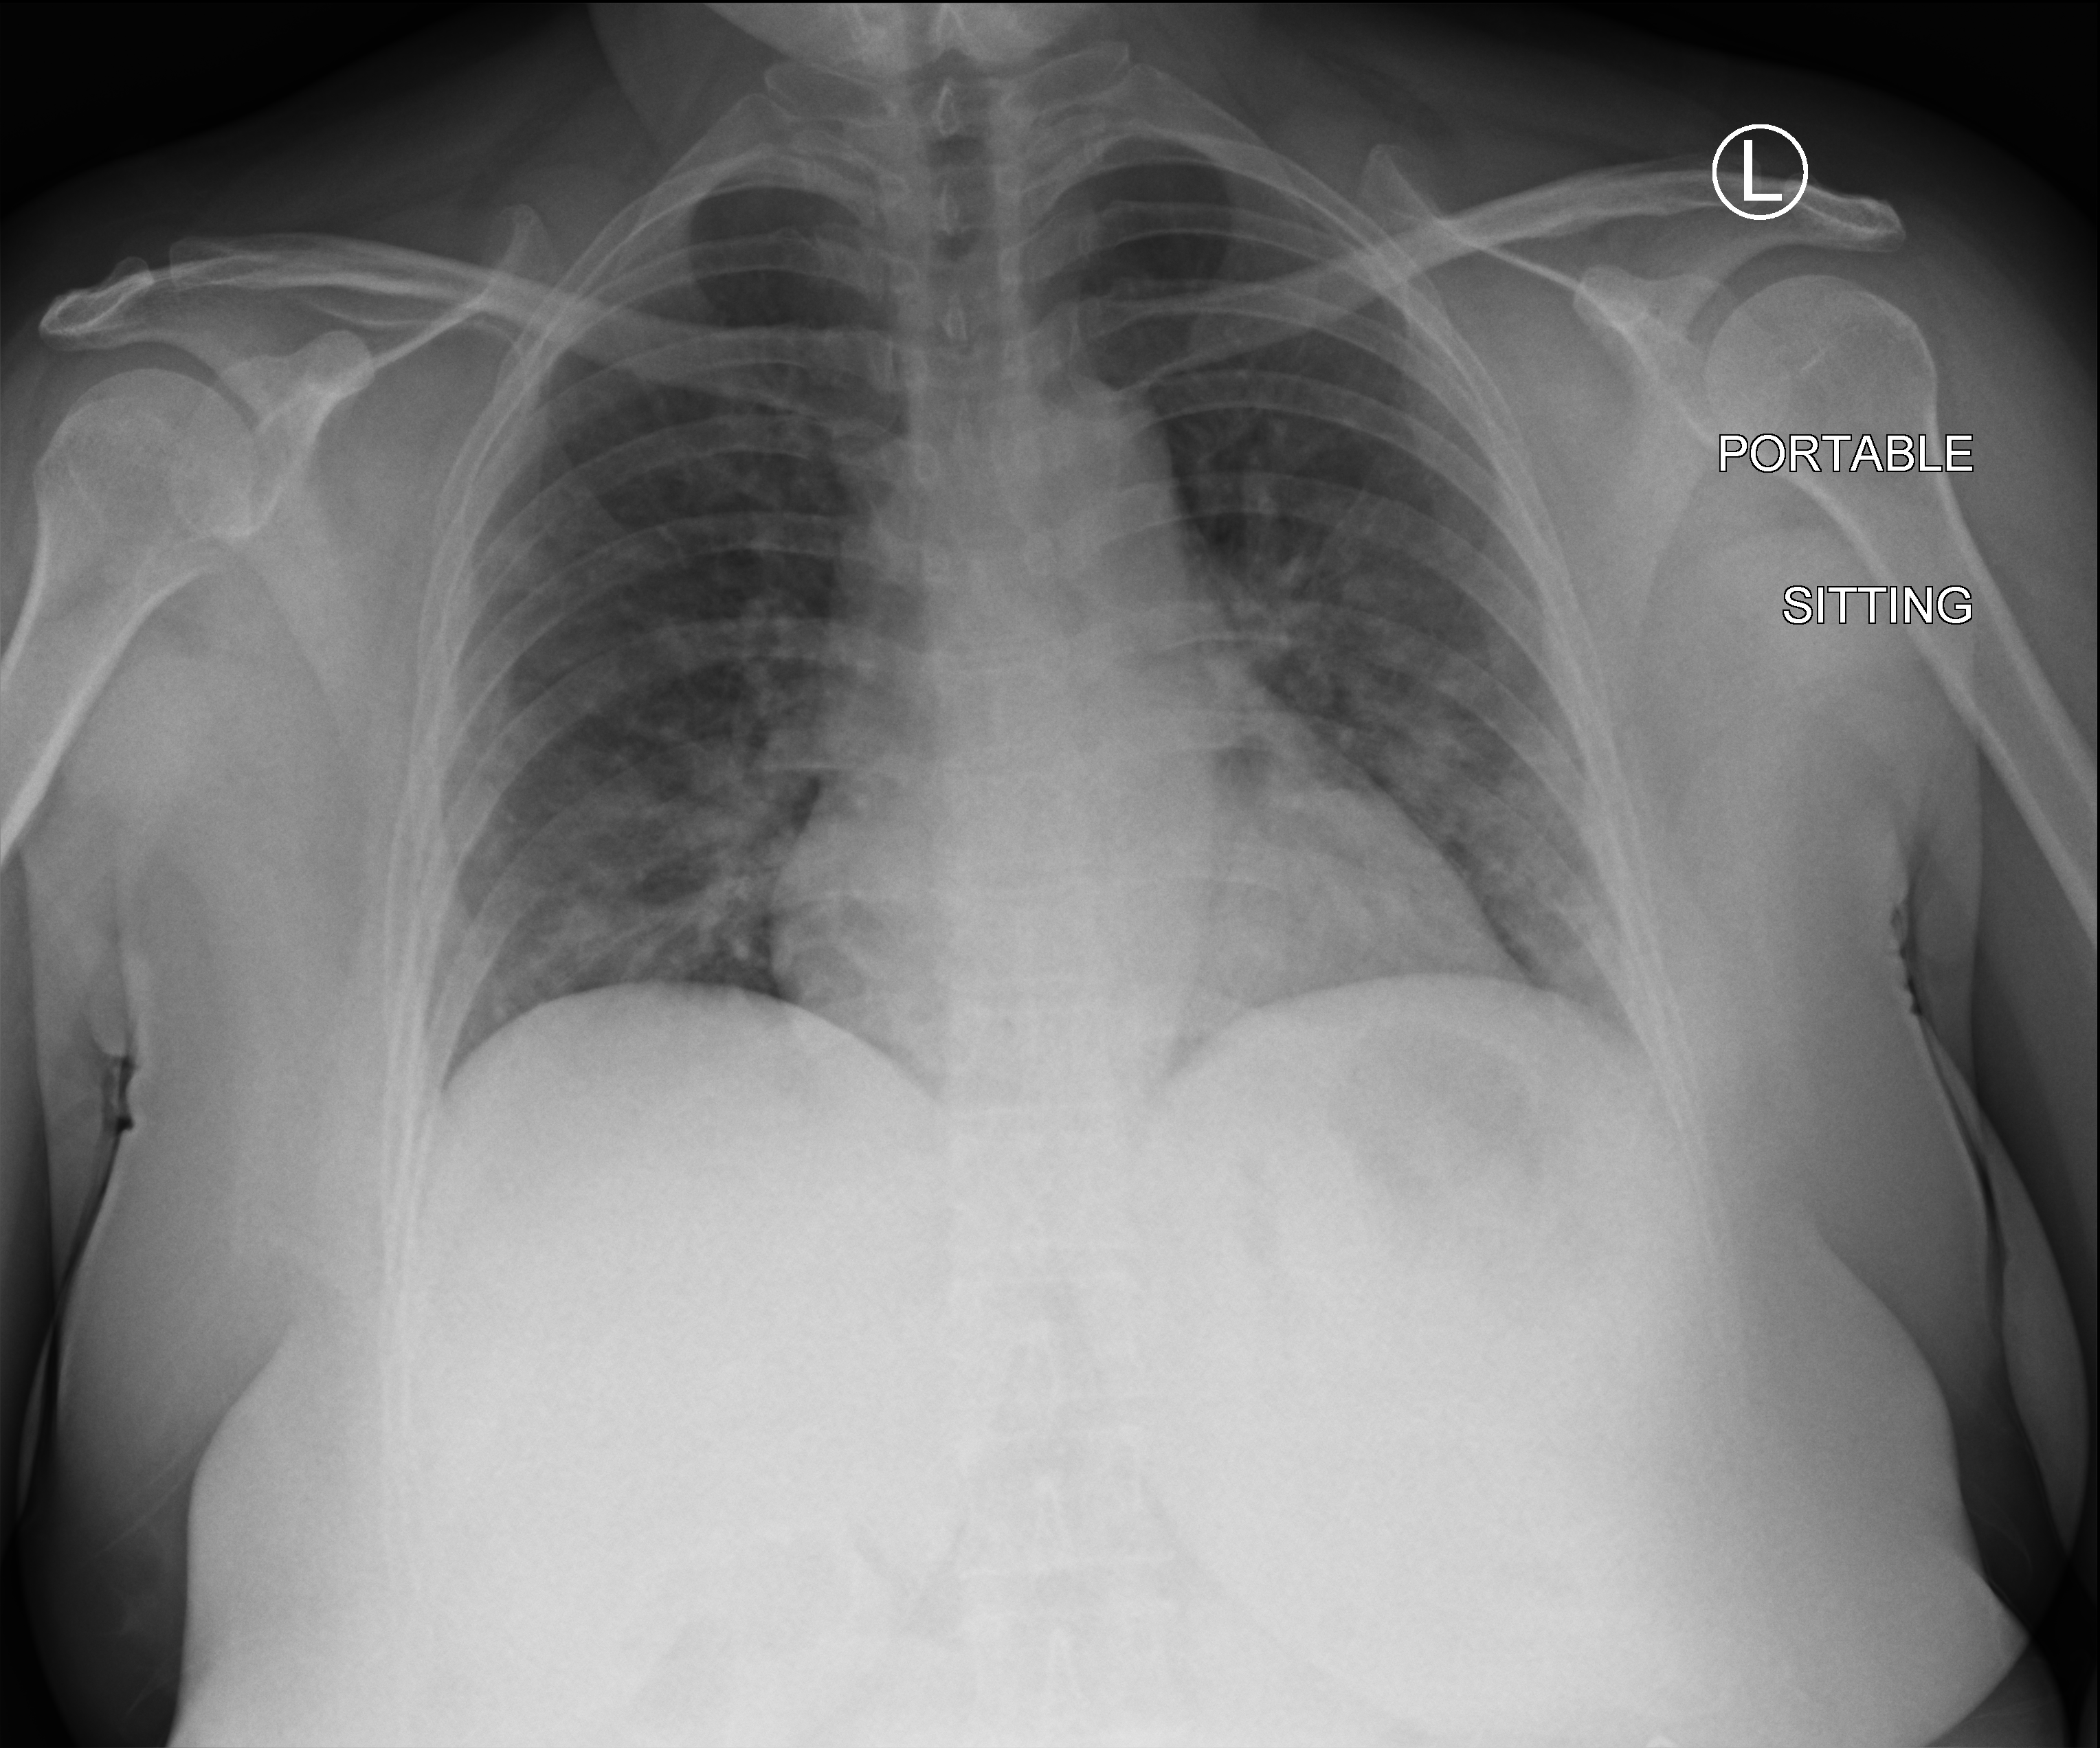
Portable chest radiograph, anteroposterior (AP) projection. Female patient hospitalised with COVID-19, age 18–59 years.
From the hospital-stay record, not from the radiograph (when in the stay this image was taken is not recorded):
- length of hospital stay: 3 days
- mechanically ventilated during this hospital stay: no
- admitted to intensive care during this hospital stay: no